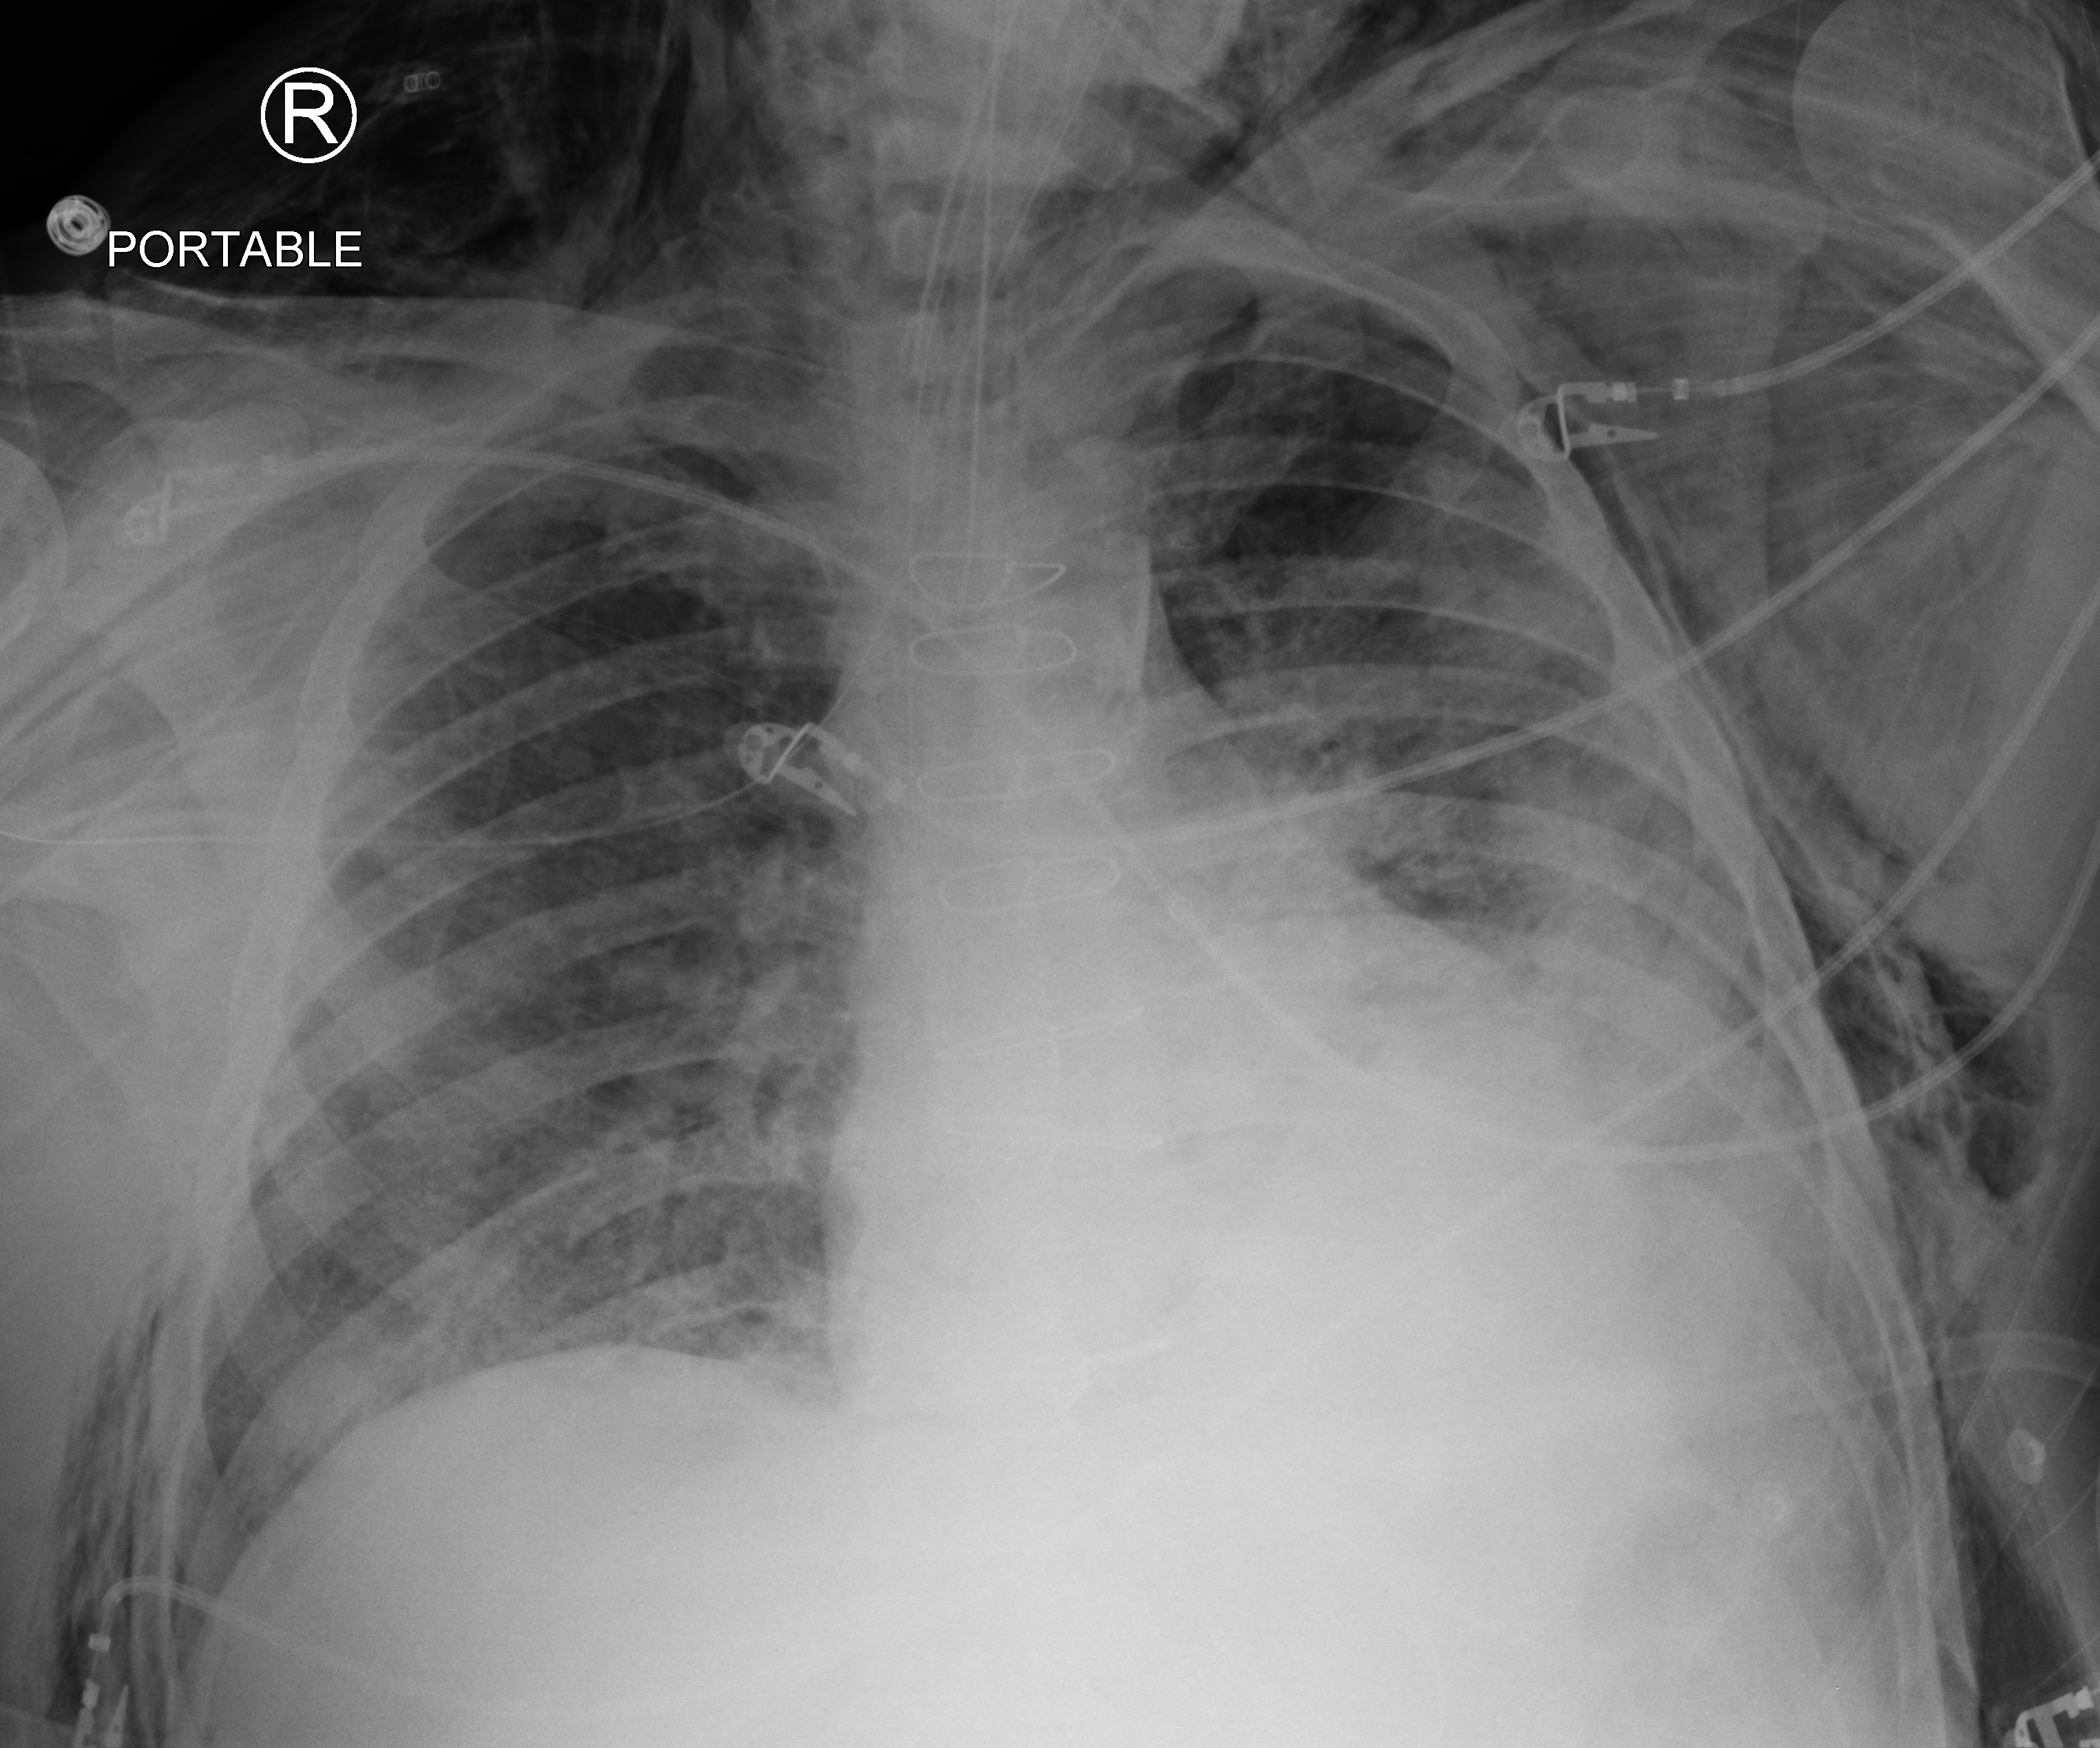
Chest X-ray (portable); anteroposterior (AP) projection. Male patient hospitalised with COVID-19, age 60–74 years.
From the hospital-stay record, not from the radiograph (when in the stay this image was taken is not recorded): admitted to intensive care during this hospital stay: yes; other chronic lung disease (admission record): no.